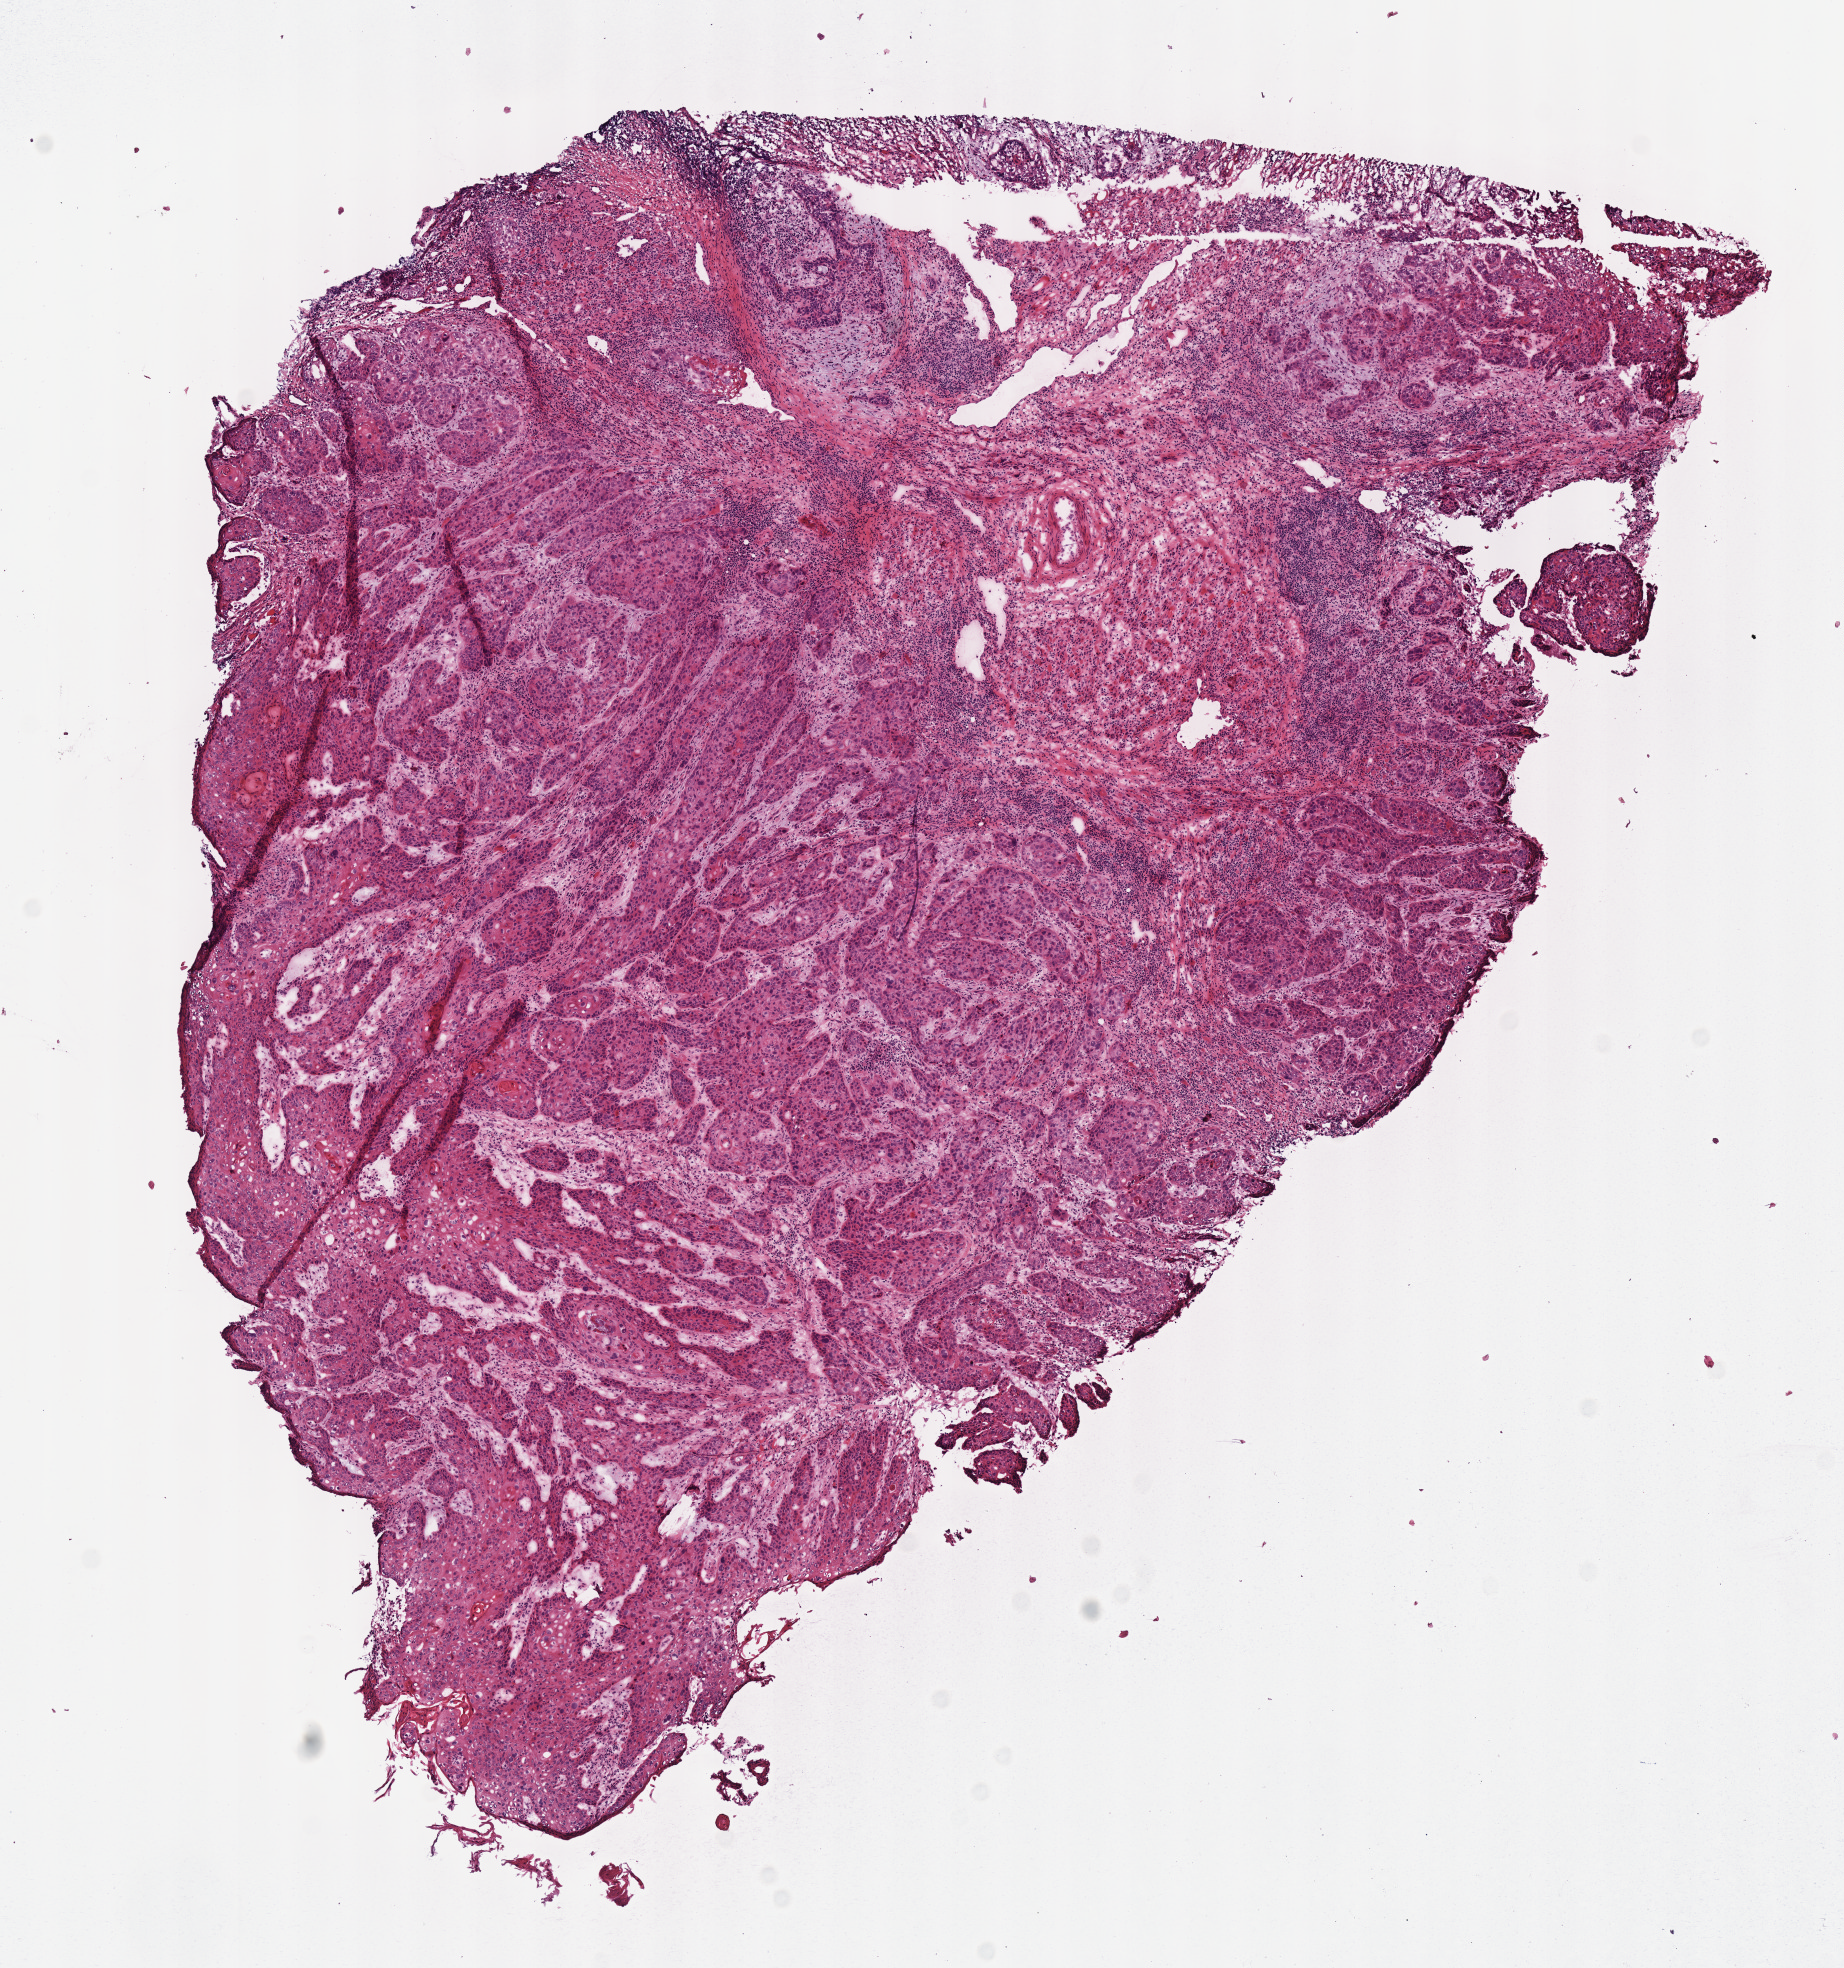
Digitized H&E-stained tissue section (whole slide), whole scanned area (about 7.3 x 7.8 mm) shown as a low-resolution overview. Frozen section. Primary tumour sample from the head and neck. Male patient; age at initial diagnosis 57 years. Histologic grade: G2 (moderately differentiated). Pathologist review of this section (percent, as recorded): tumour cells 85%, tumour nuclei 75%, normal cells 0%, stromal cells 15%, necrosis 0%. Infiltration values recorded for this section: lymphocyte infiltration 15%.
• histologic diagnosis: Squamous cell carcinoma, NOS (tongue, NOS)
• laterality: left
• lymph nodes positive (case pathology): 3 of 42 examined